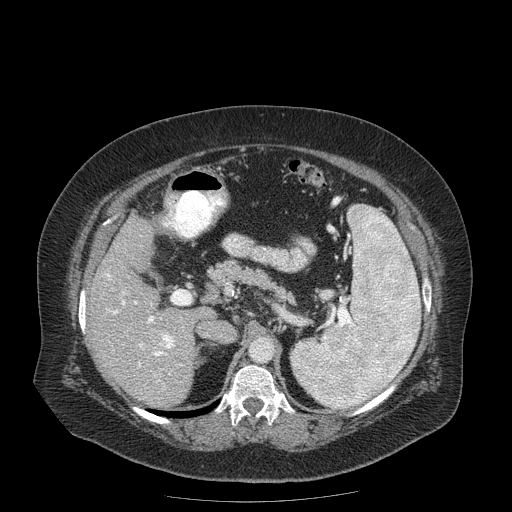
Contrast-enhanced abdominal CT (liver protocol), one axial slice; position 101 of 204 along the scan axis; reconstruction kernel STANDARD; 120 kVp; soft-tissue window (W 400 / L 40 HU); 512 × 512 image matrix, field of view 440 × 440 mm. Case-level facts recorded for this patient, not image findings: diagnosis: hepatocellular carcinoma (patient treated with transarterial chemoembolisation; whether this scan precedes or follows treatment is not stated here); TNM stage (as recorded): Stage-IIIB.
Annotated regions visible in this slice (semi-automatically segmented with operator editing):
- liver parenchyma outside the tumour (the mass and vessels are separate outlines, so this box may not span the whole liver): bounding box (x1, y1, x2, y2) in pixels: (90, 214, 198, 408)
- liver vessels: (105, 273, 175, 366)